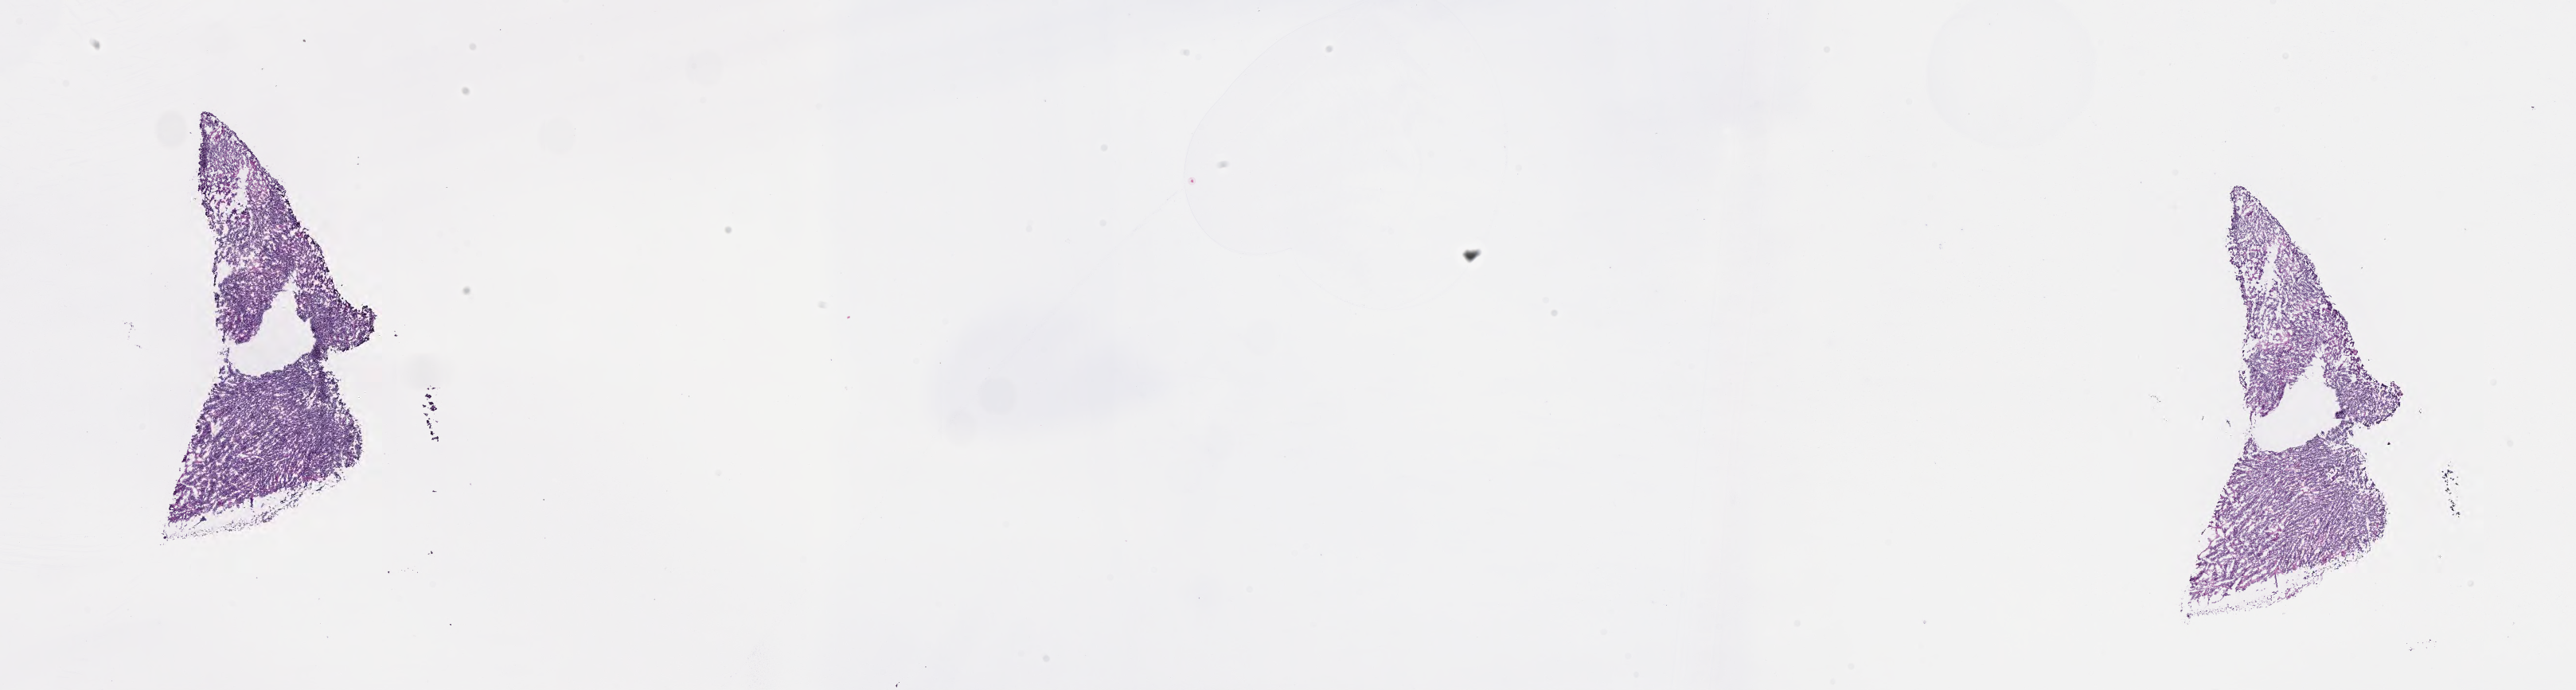
Whole-slide image, hematoxylin and eosin (H&E) stain of tumor tissue from the eye — whole scanned area (about 26.2 x 7.0 mm) shown as a low-resolution overview, cryosection (OCT / tissue freezing medium). Patient: female, age 662 days.
Diagnosis: Retinoblastoma, NOS.